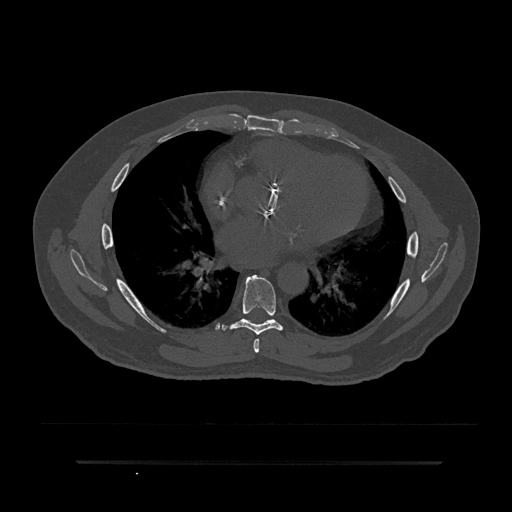
CT including the spine, one axial slice; position 481 of 797 along the scan axis; 120 kVp; bone window (W 1800 / L 400 HU); 512 × 512 image matrix, field of view 464 × 464 mm. Male patient, age 59 years. From the clinical record (not read from this slice): primary cancer: bile ducts.
Annotated regions visible in this slice (semi-automatically segmented with operator editing):
- T6 vertebra: bounding box (x1, y1, x2, y2) in pixels: (253, 338, 260, 353)
- T7 vertebra: (222, 275, 284, 335)